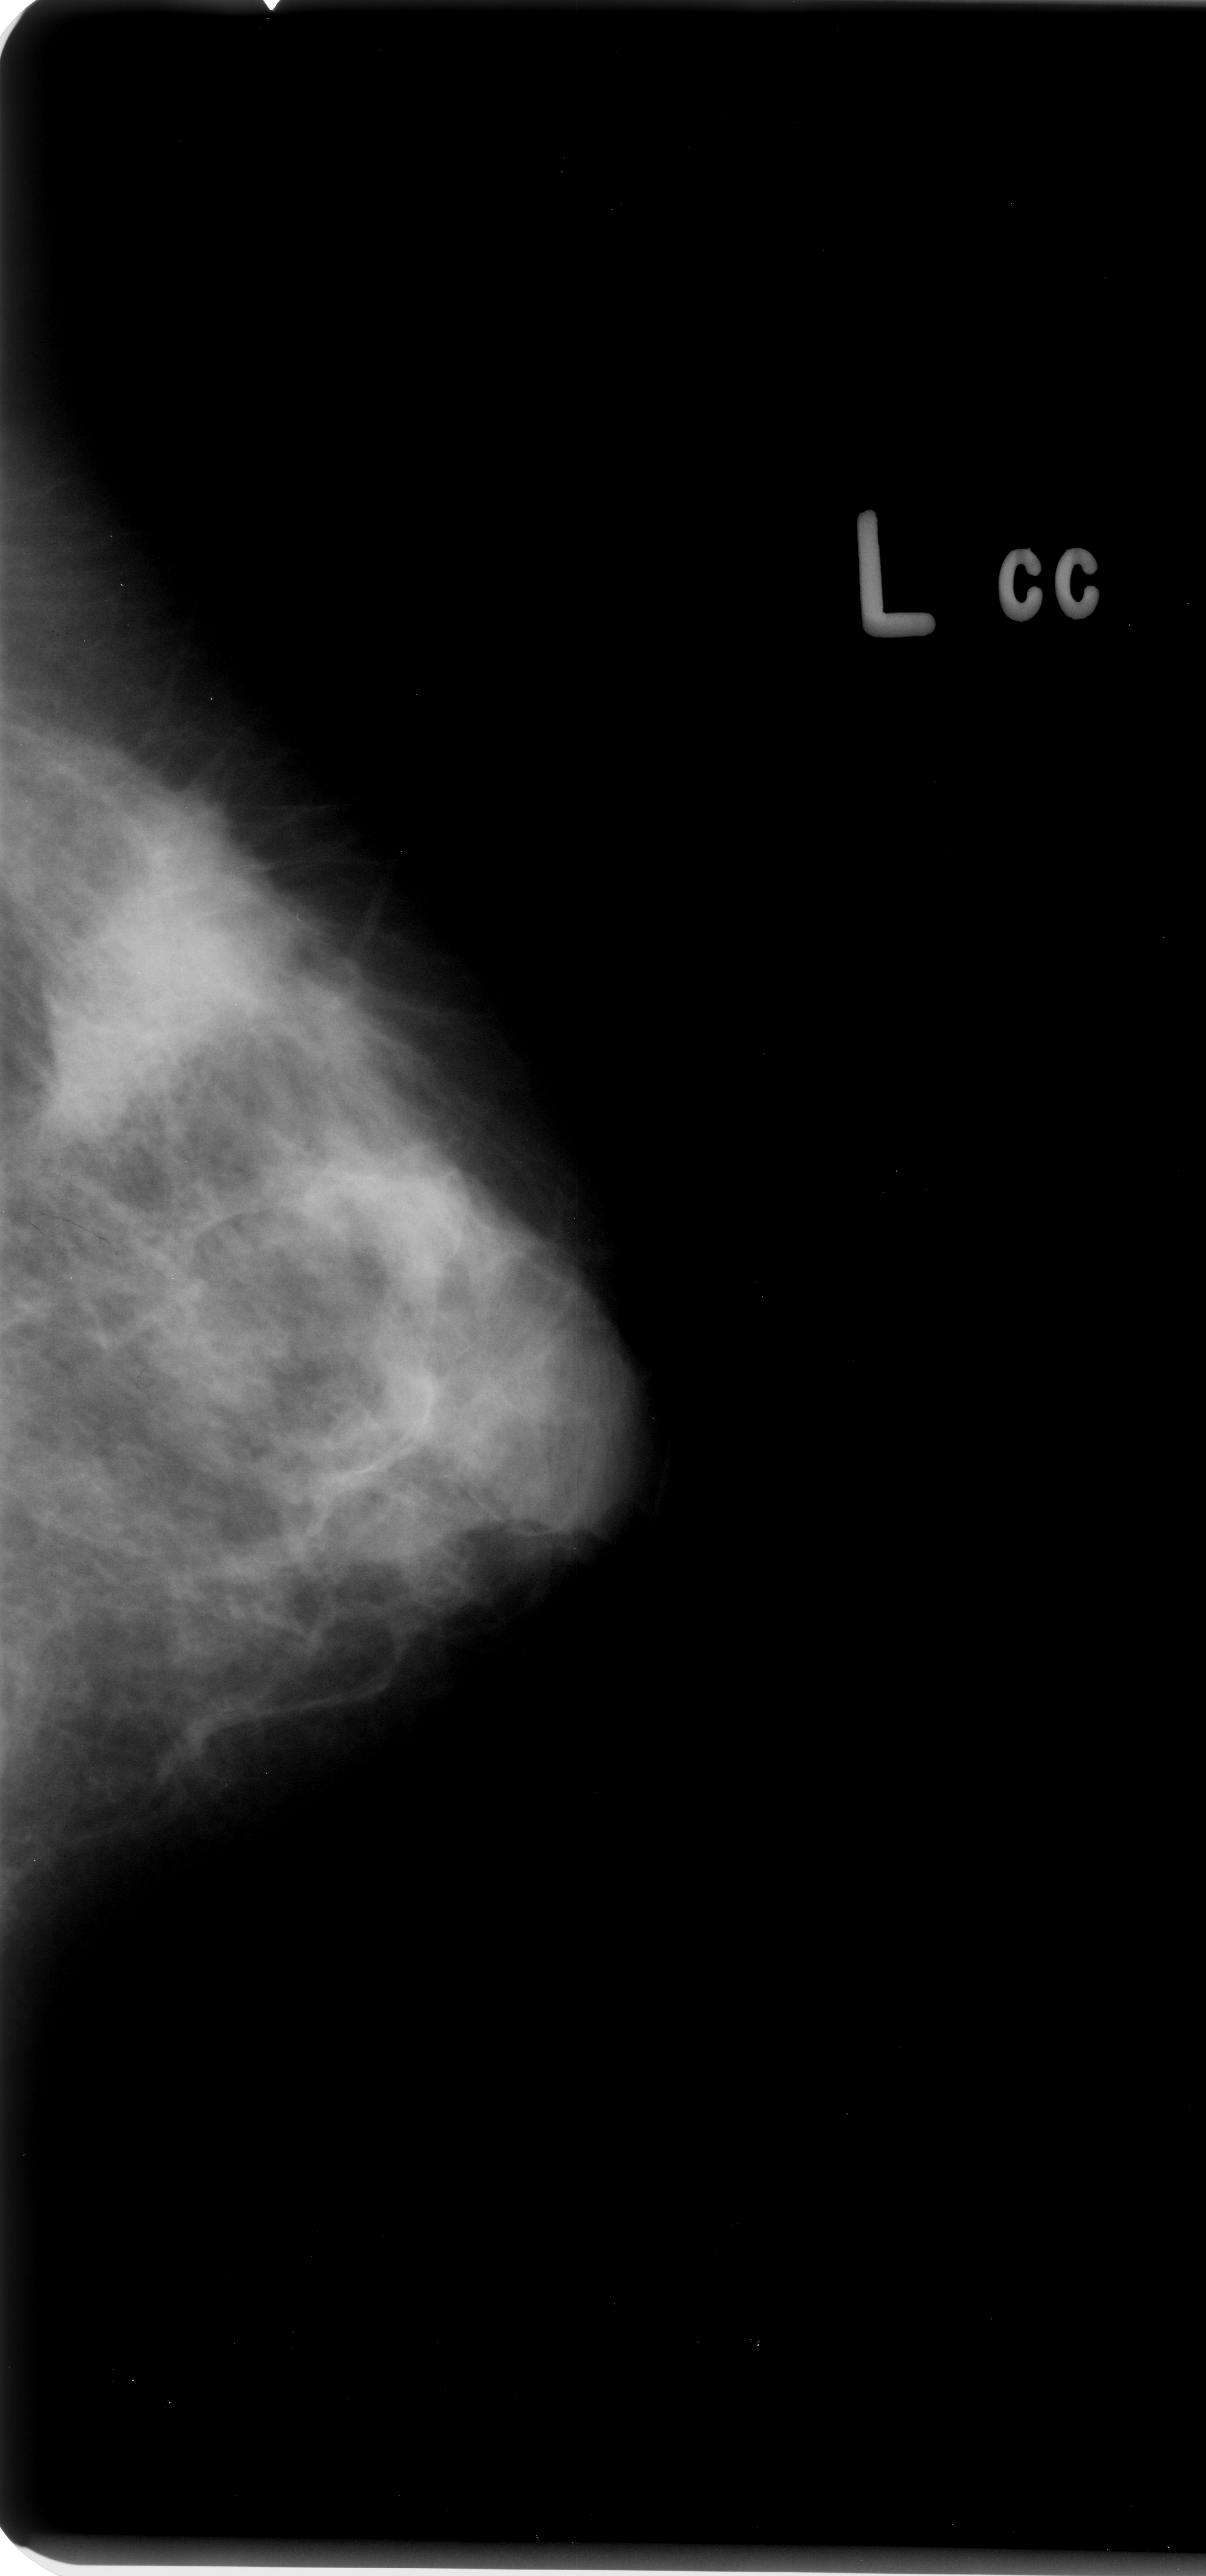
Mammogram (digitized film). Left breast. CC view. BI-RADS breast density category 3 (scale 1–4). 1206 × 2576 image matrix.
Marked abnormalities (boxes around the expert regions of interest):
- calcifications, morphology amorphous / round and regular, distribution clustered; BI-RADS assessment category 4; subtlety rating 4 on a 1 (subtle) to 5 (obvious) scale; pathology result (as recorded, not read from the image): malignant: bounding box [x1, y1, x2, y2] px = [124, 1056, 164, 1104]